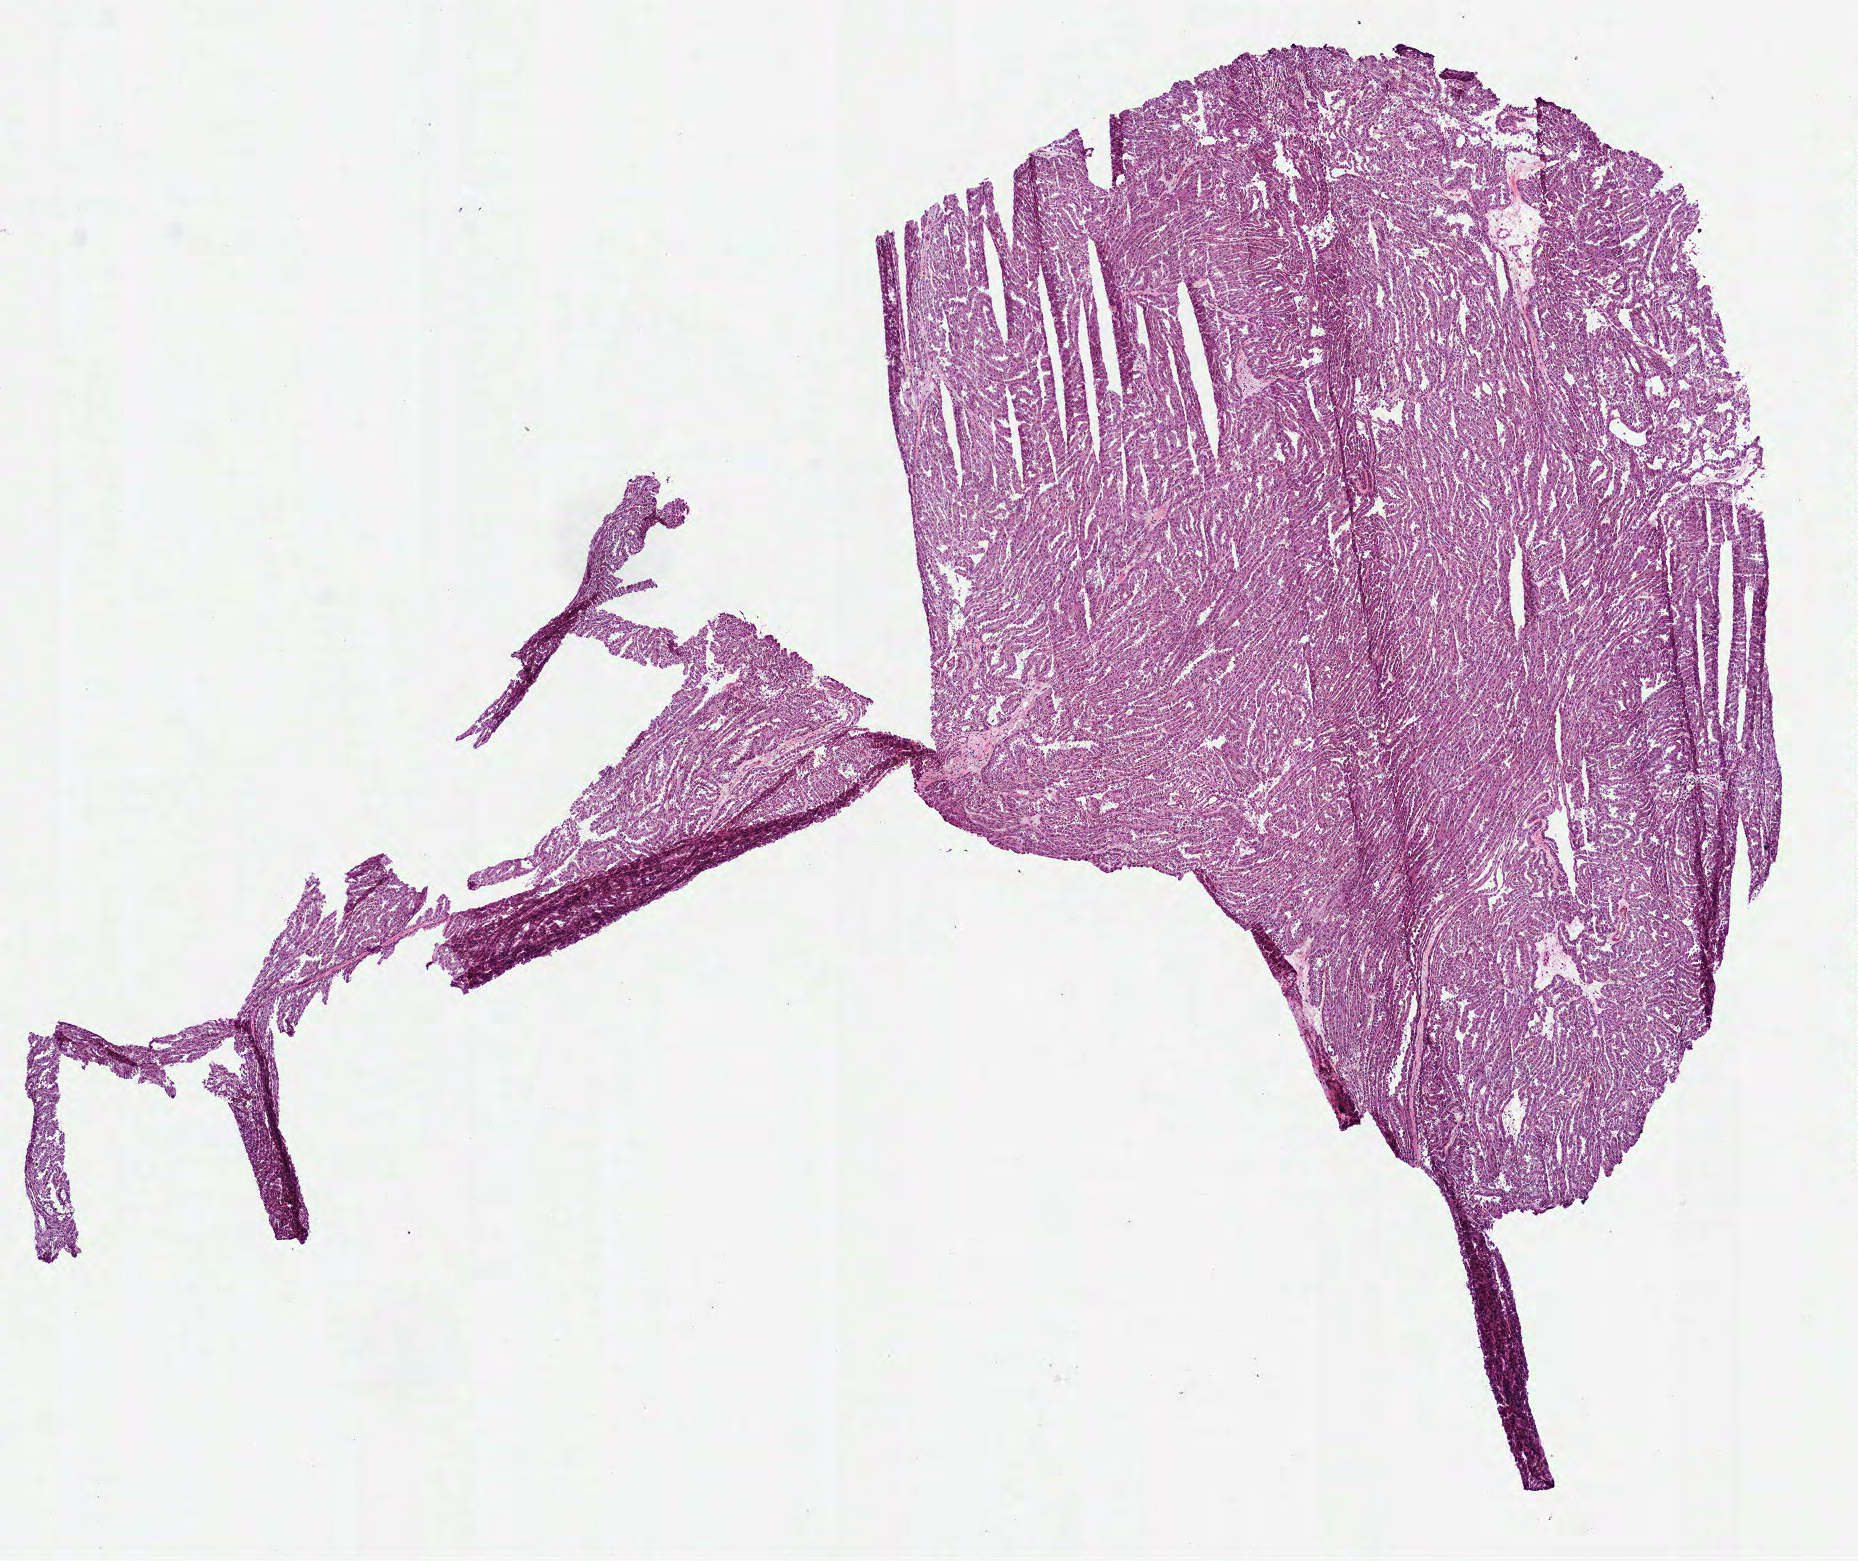
Digitized H&E-stained tissue section (whole slide), low-resolution overview of the scanned area, about 7.5 x 6.3 mm (slide scanned at 40x), frozen section from the bottom of the tissue portion, primary tumour sample from the kidney. Patient: male, age at initial diagnosis 63 years. Composition of this section per pathologist review: tumour cells 95%, tumour nuclei 95%, normal cells 0%, stromal cells 5%, necrosis 0%.
TNM: T1b NX MX. Histologic diagnosis: Papillary adenocarcinoma, NOS. AJCC pathologic stage: I (7th edition).